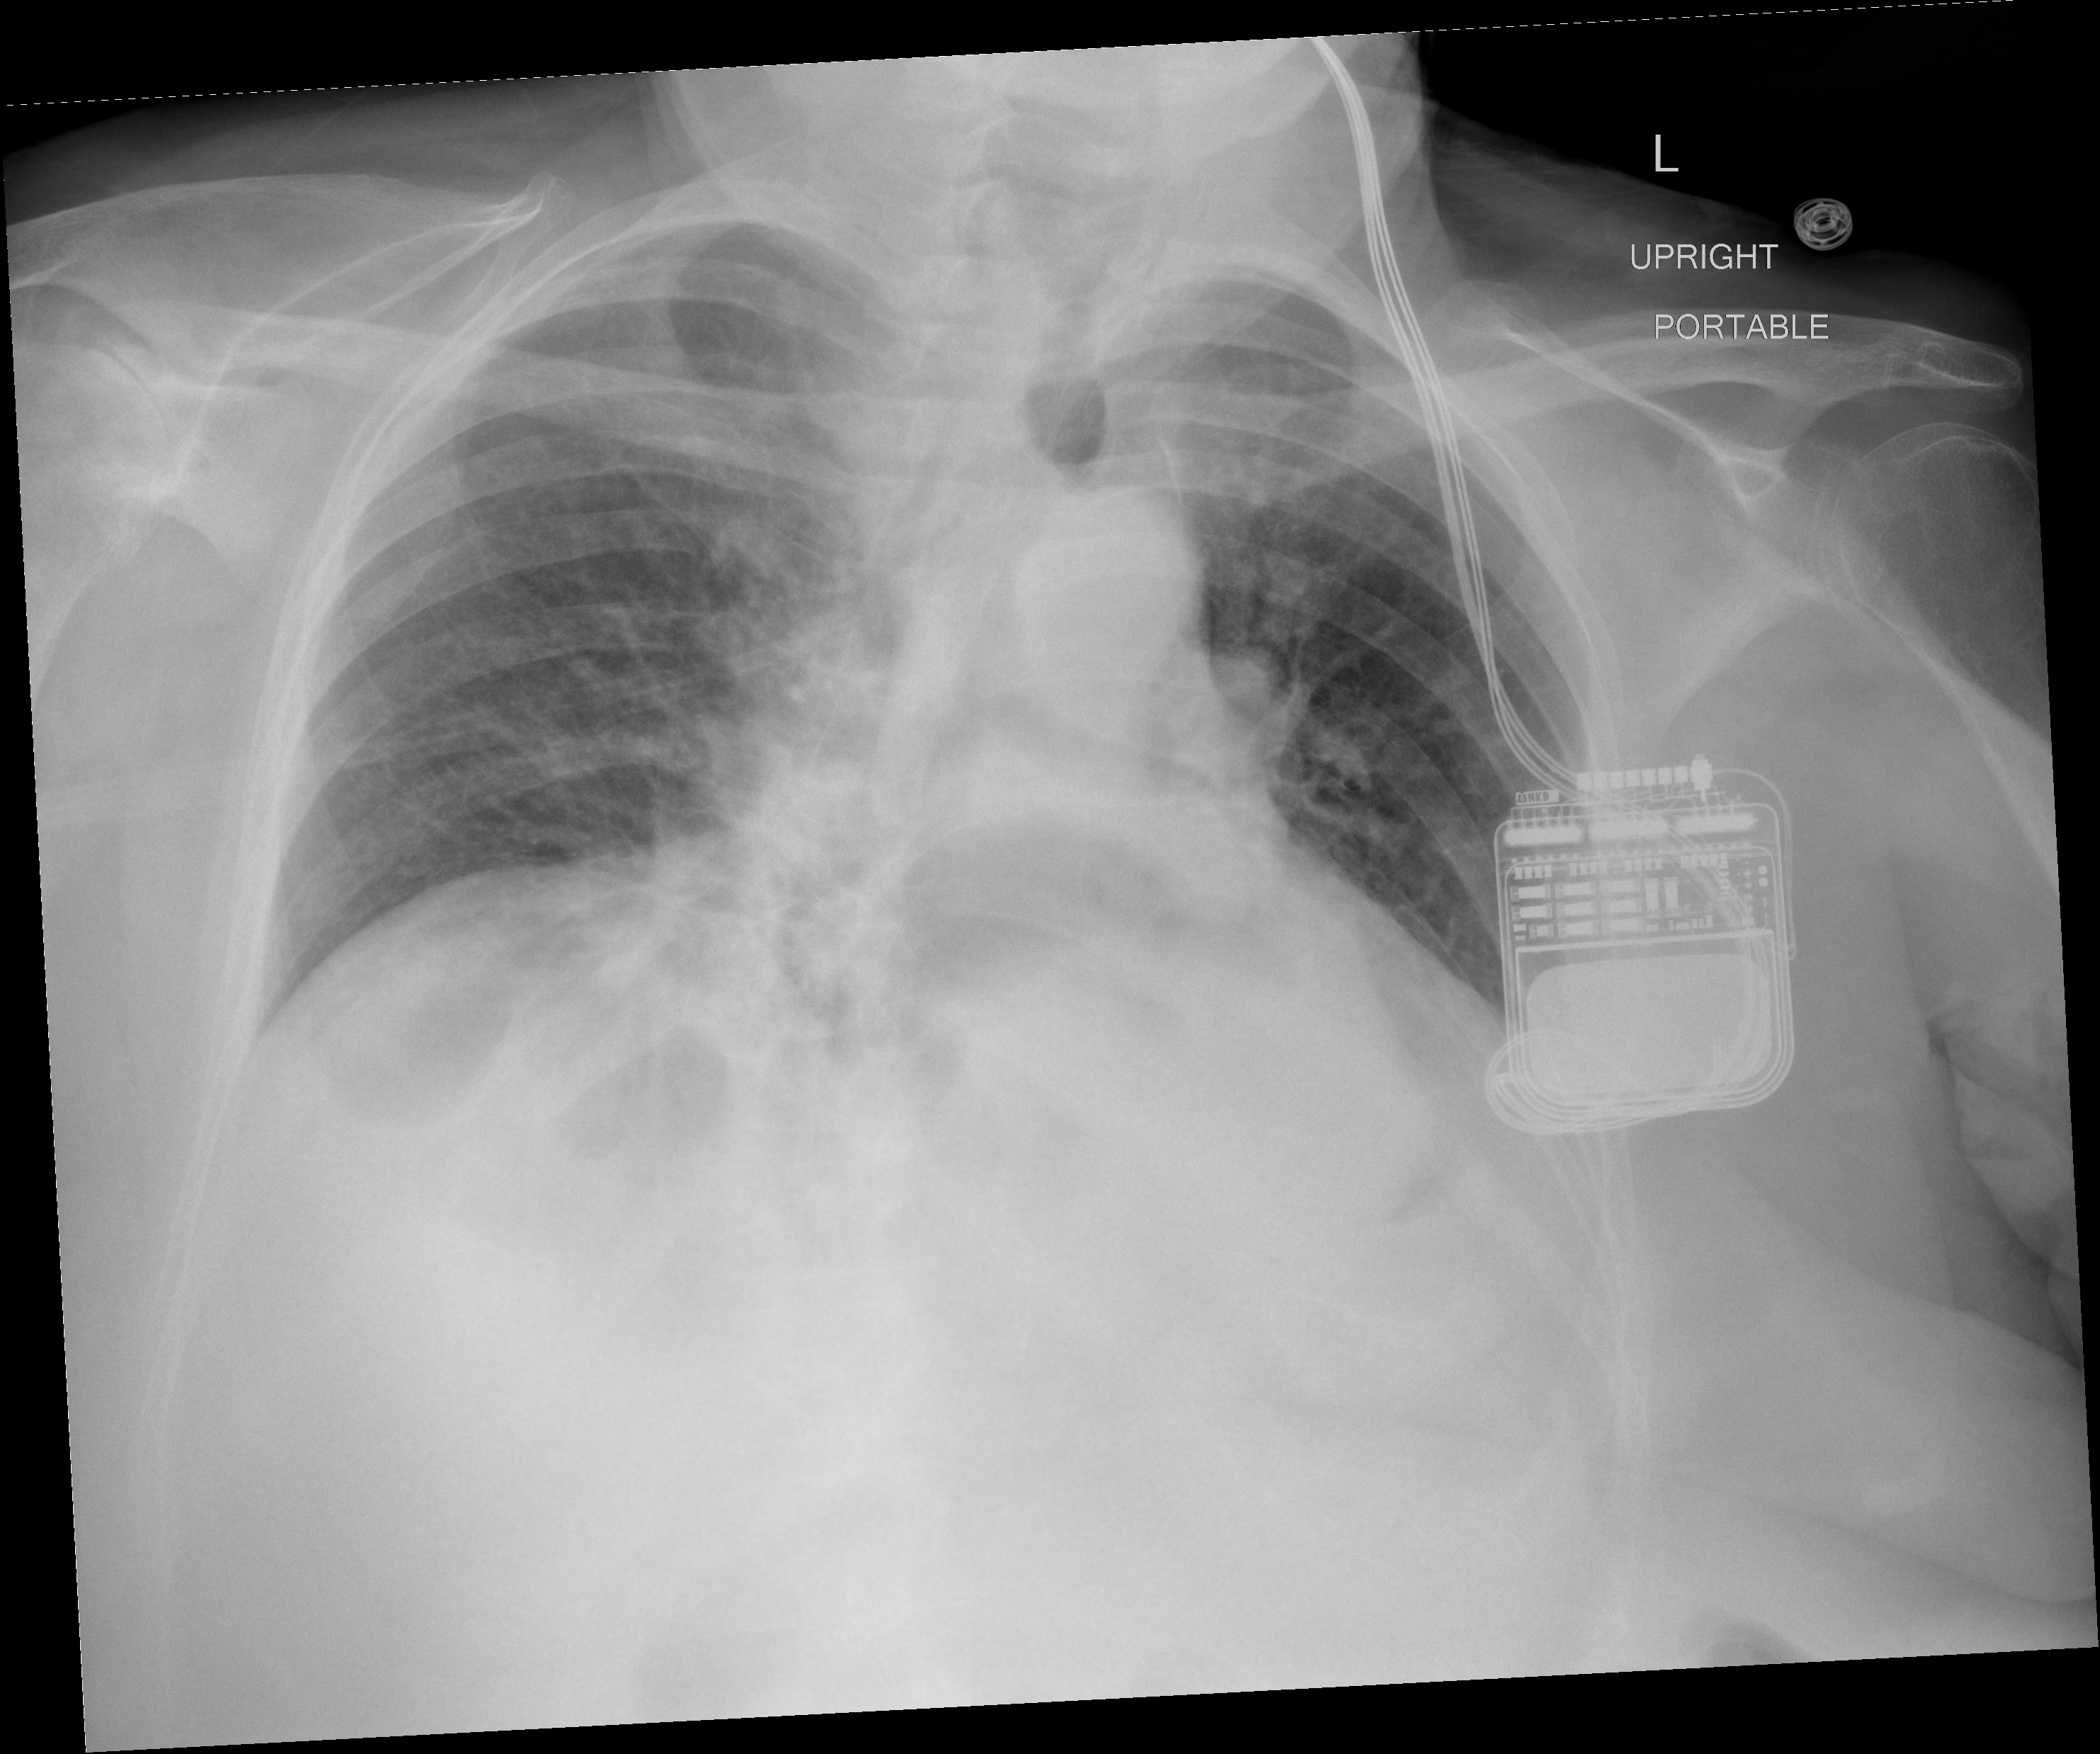
Portable chest radiograph, AP projection. Female patient, age 81 years; imaged 0 days after the COVID-19 diagnosis.
Radiologist's key findings for this exam: patchy bibasilar opacities.